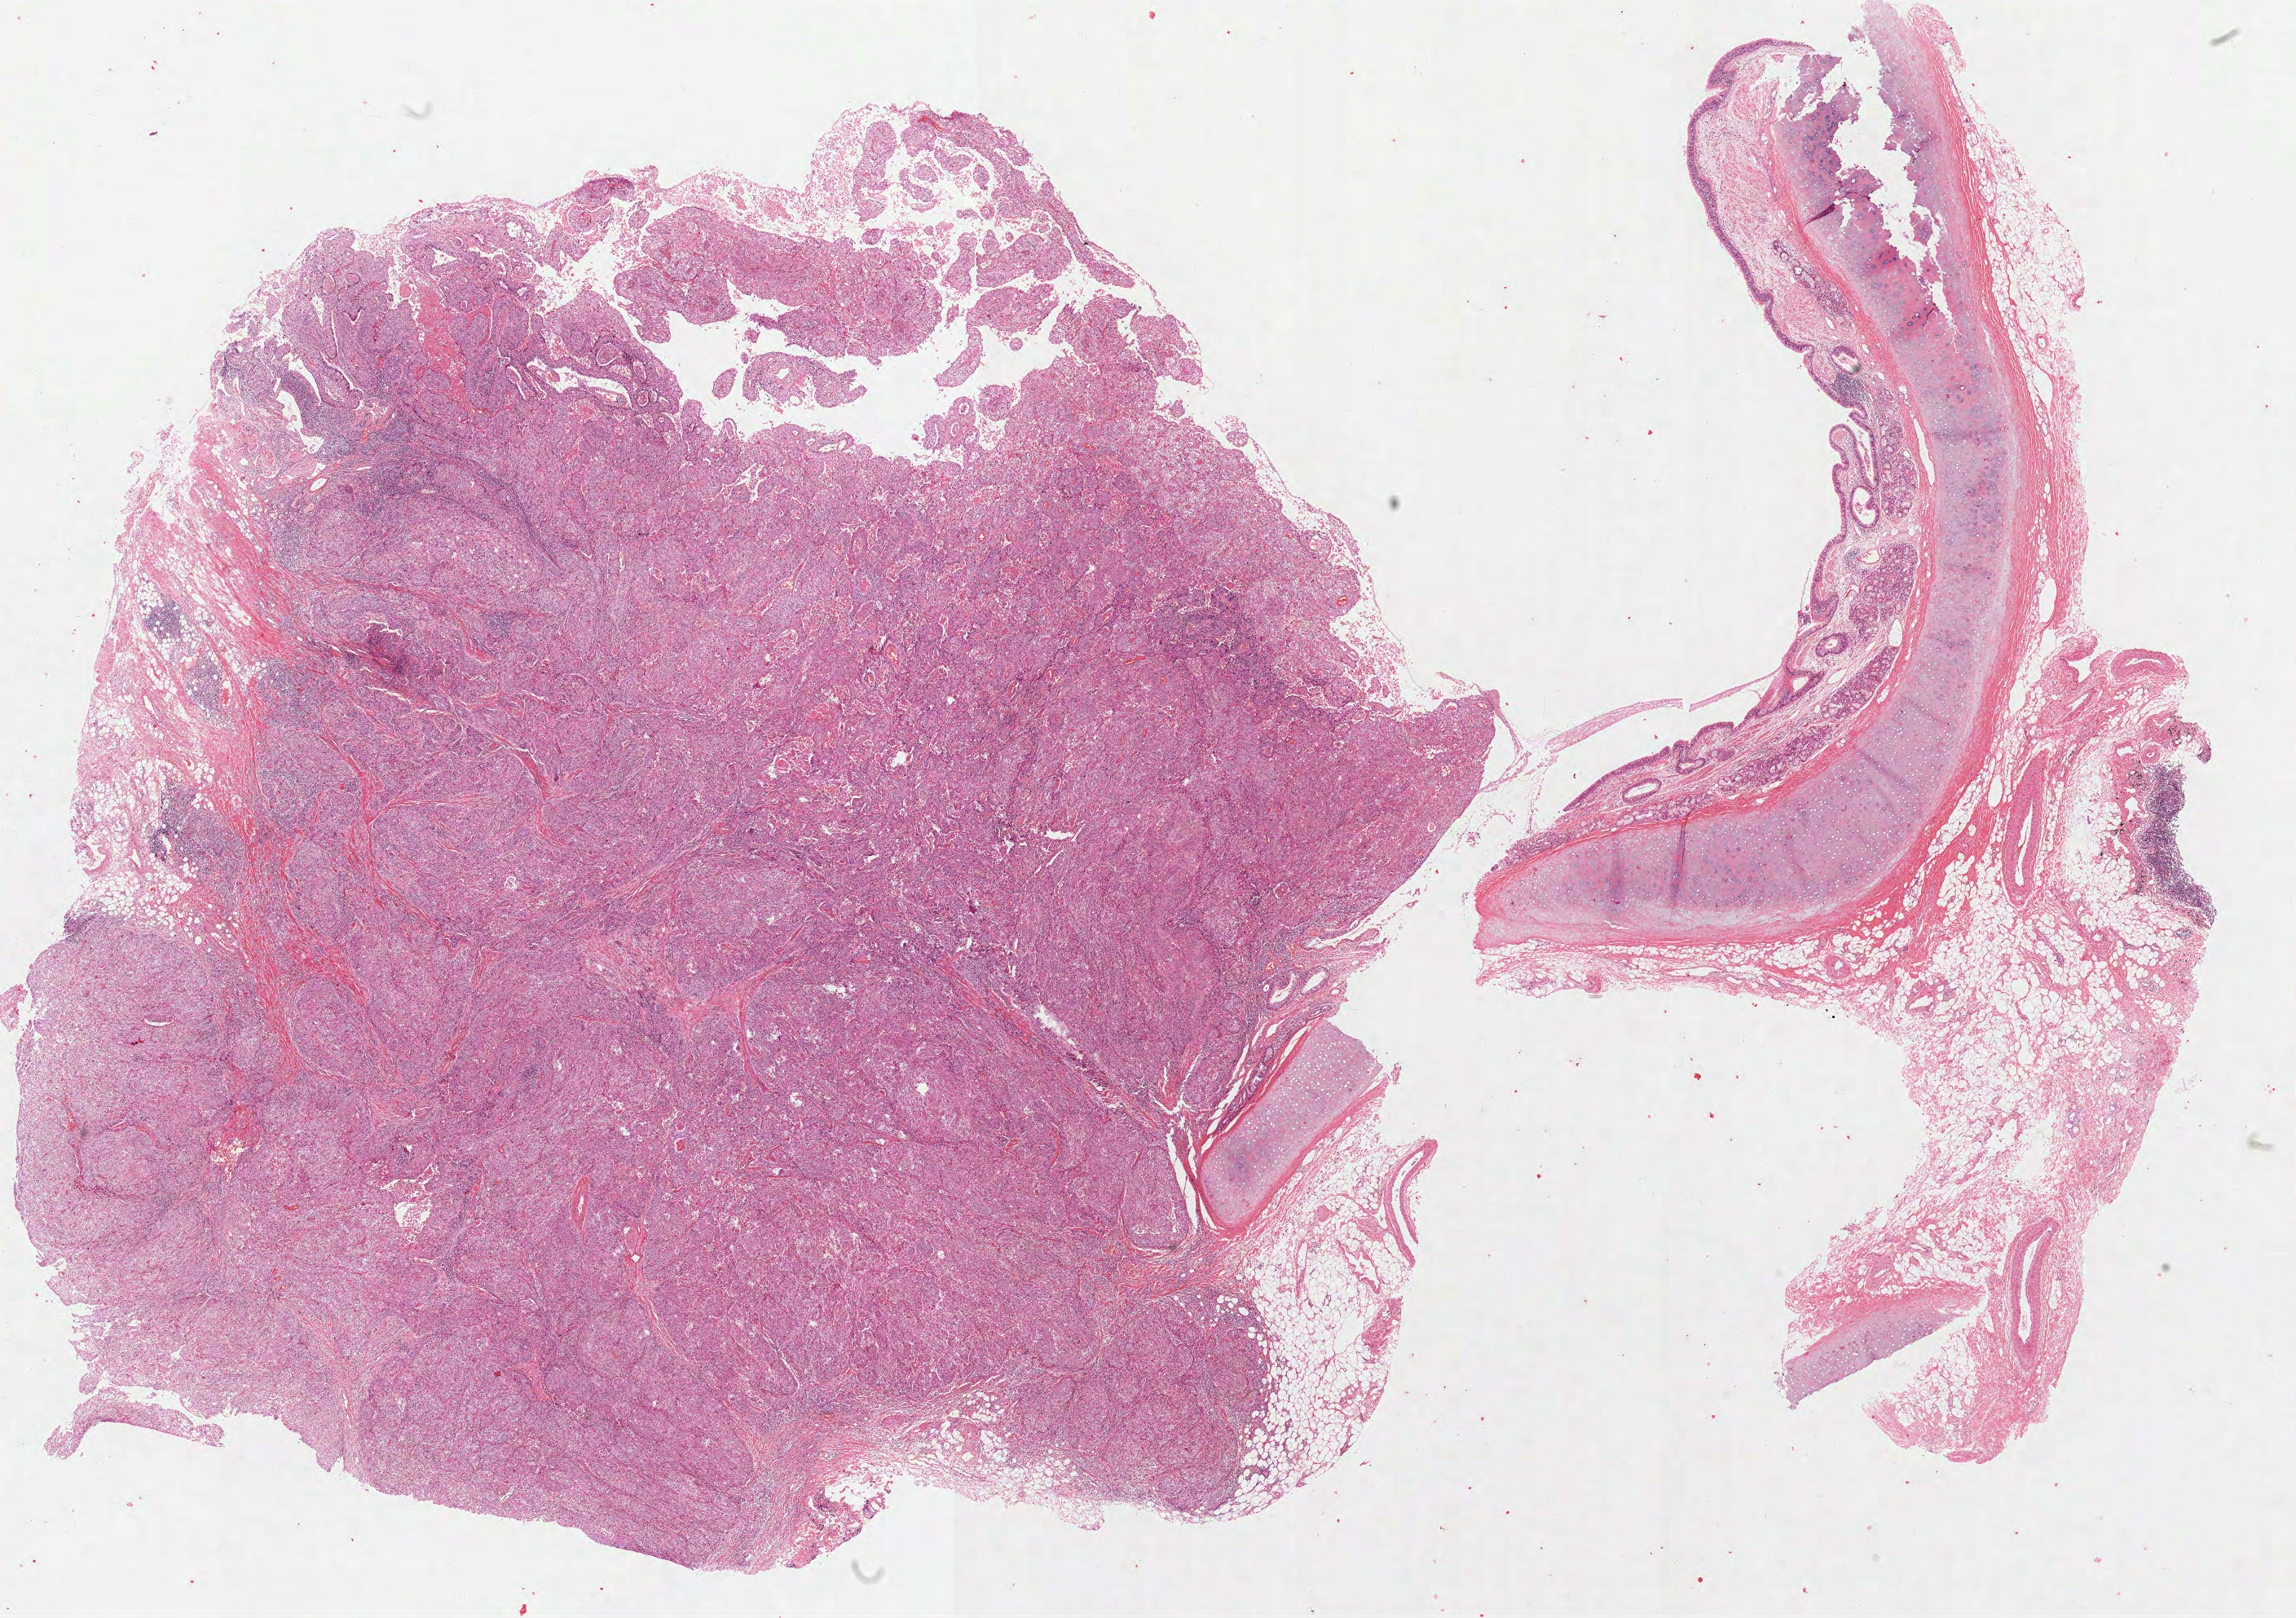
Digitized Hematoxylin and eosin (H&E) stained tissue section (whole slide), shown as a low-resolution overview of the whole scanned area (about 22.7 x 16.0 mm). Formalin-fixed paraffin-embedded (FFPE) diagnostic section. Primary tumour sample from the lung. Male patient; age at initial diagnosis 63 years.
Laterality: left. Diagnosis: Squamous cell carcinoma, NOS (upper lobe, lung). TNM: T1a N0 M0. AJCC pathologic stage: IA (7th edition).